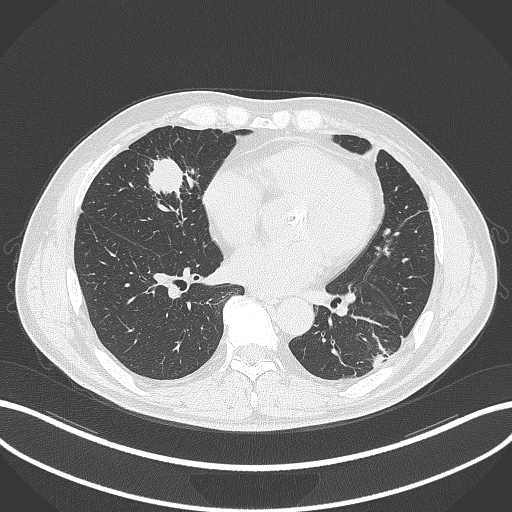
Chest CT, one axial slice. Slice 116 of 399 in the series (ordered by position). Reconstruction kernel B70f. 120 kVp. Lung window (W 1500 / L -600 HU). 1 mm slice thickness. 512 × 512 image matrix, field of view 400 × 400 mm. Patient: male, 59 years. Case-level facts recorded for this patient, not image findings: clinical TNM (as recorded): T2a N1 M0.
Annotated regions visible in this slice (rectangle marked by the reading radiologist):
- lung tumour (recorded histology: adenocarcinoma): bounding box <146,154,190,200> (left, top, right, bottom; pixels)